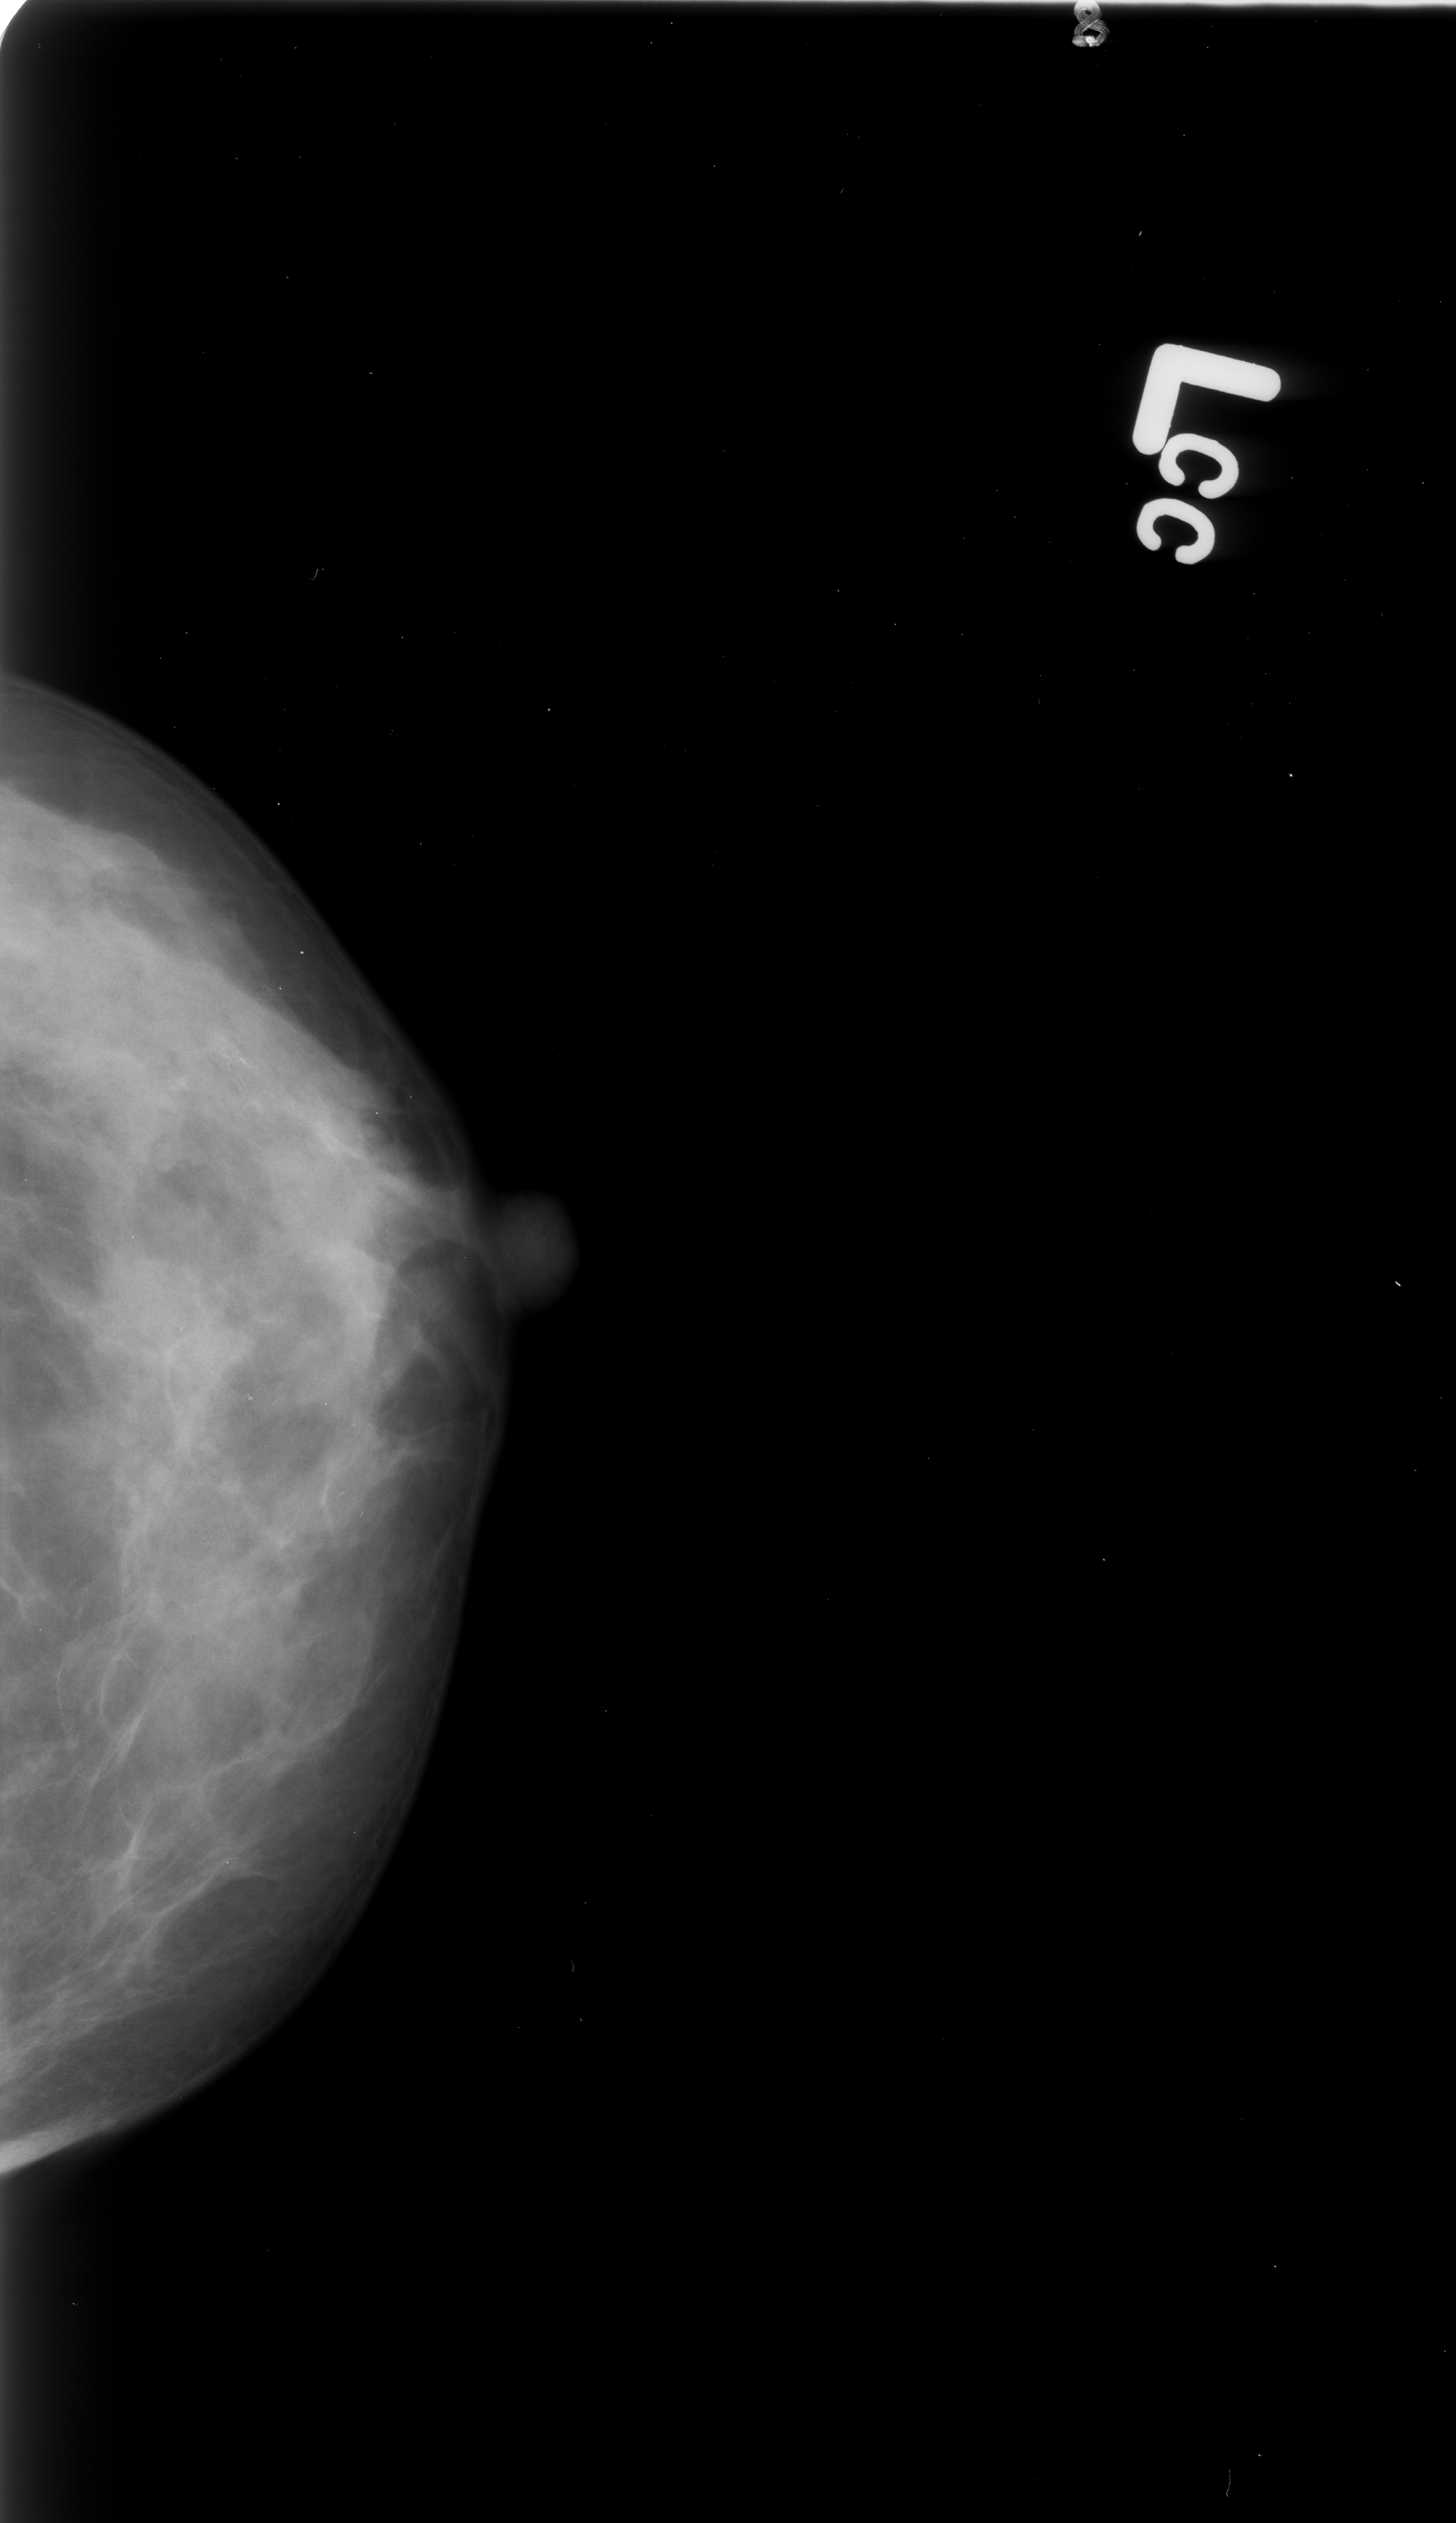
Scanned film-screen mammogram; left breast; CC view; breast composition: heterogeneously dense (BI-RADS density category 3 of 4).
Radiologist-marked abnormalities on this image: calcifications, morphology punctate / amorphous, distribution clustered / linear; BI-RADS assessment category 4; pathology (as recorded): benign.